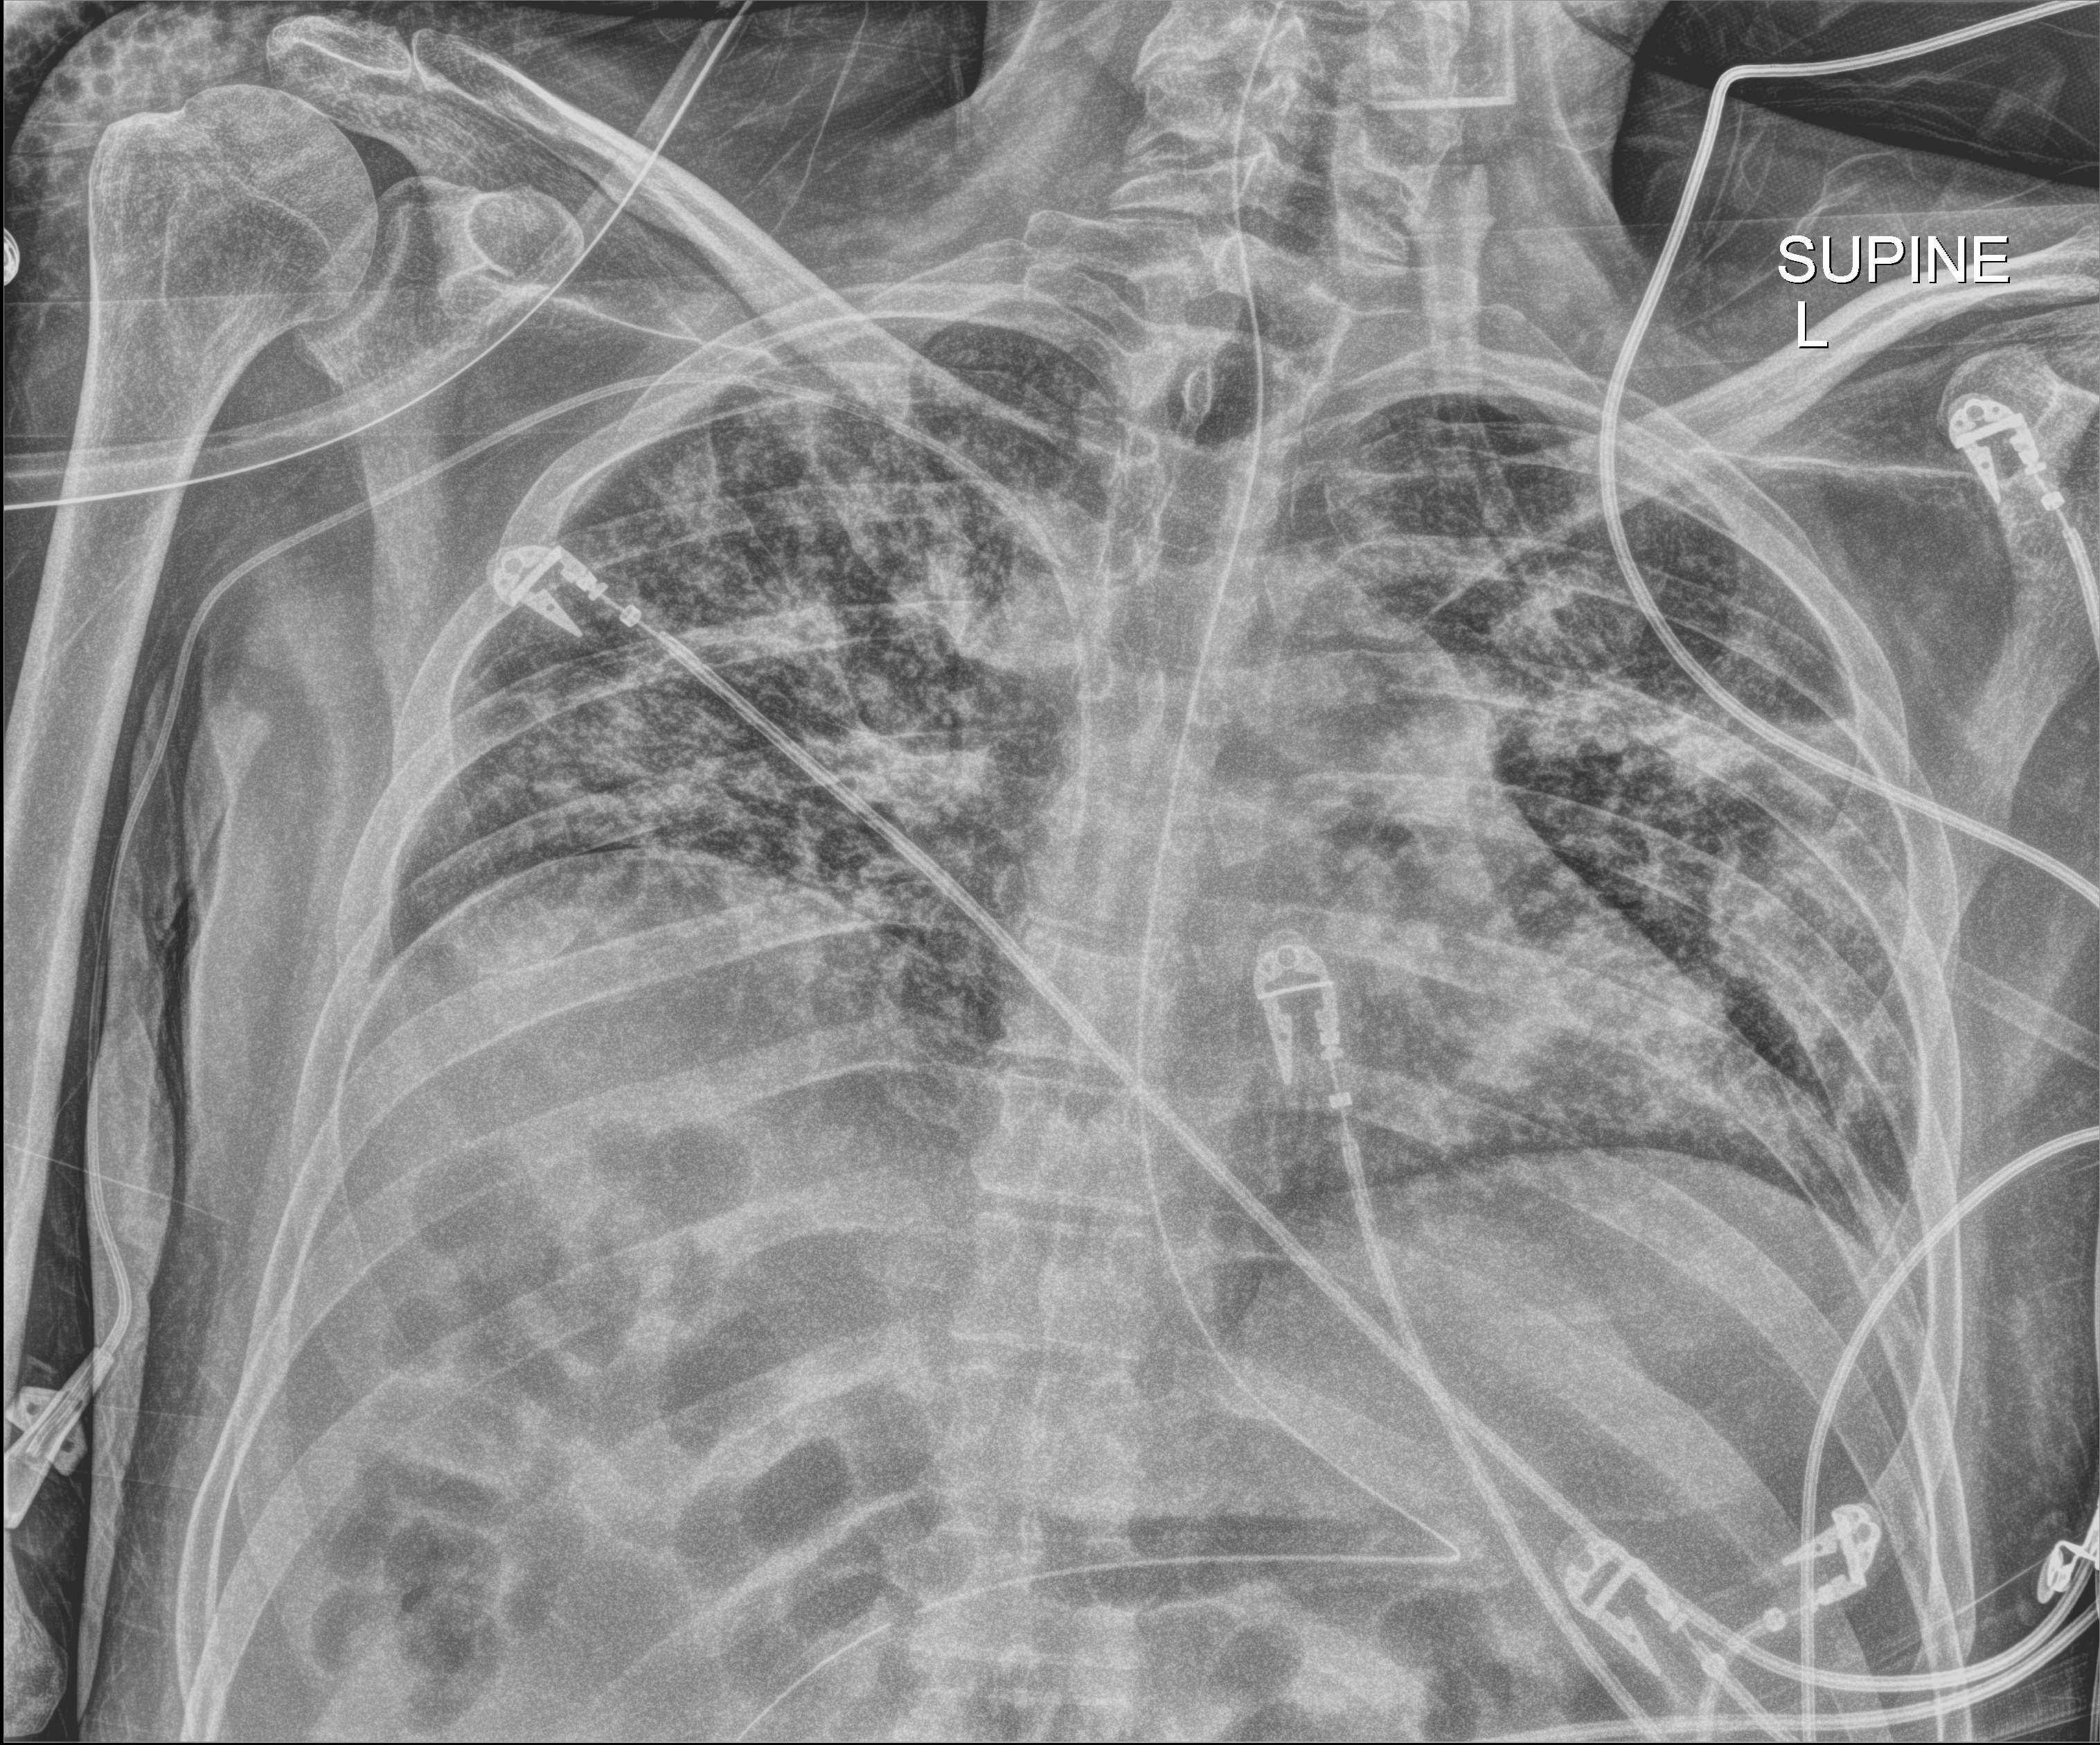
Chest X-ray (portable); anteroposterior (AP) projection. Male patient hospitalised with COVID-19, age 18–59 years.
Hospital-stay facts (about this admission, not read from this image; timing relative to this image not recorded):
- admitted to intensive care during this hospital stay: yes
- COPD (admission record): no